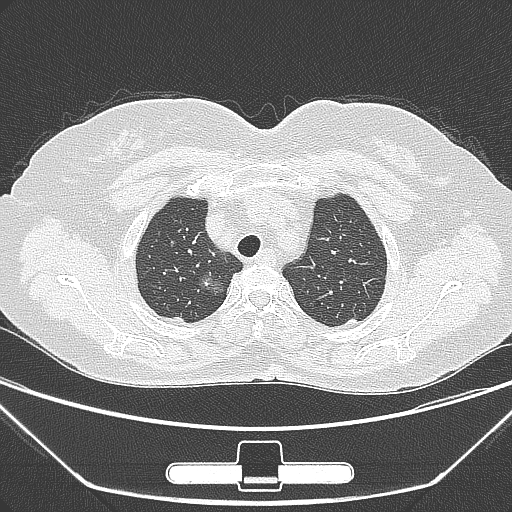
Chest CT, one axial slice. Position 232 of 275 along the scan axis. Lung window (W 1500 / L -600 HU). 1 mm slice thickness. 512 × 512 image matrix, field of view 356 × 356 mm. Female patient, age 63 years. Case-level facts recorded for this patient, not image findings: clinical TNM (as recorded): T1a N0 M0; histopathological grade: G1.
Annotated regions visible in this slice (bounding box drawn by a radiologist):
- lung tumour (recorded histology: adenocarcinoma): bounding box (x1, y1, x2, y2) in pixels: (191, 266, 241, 315)